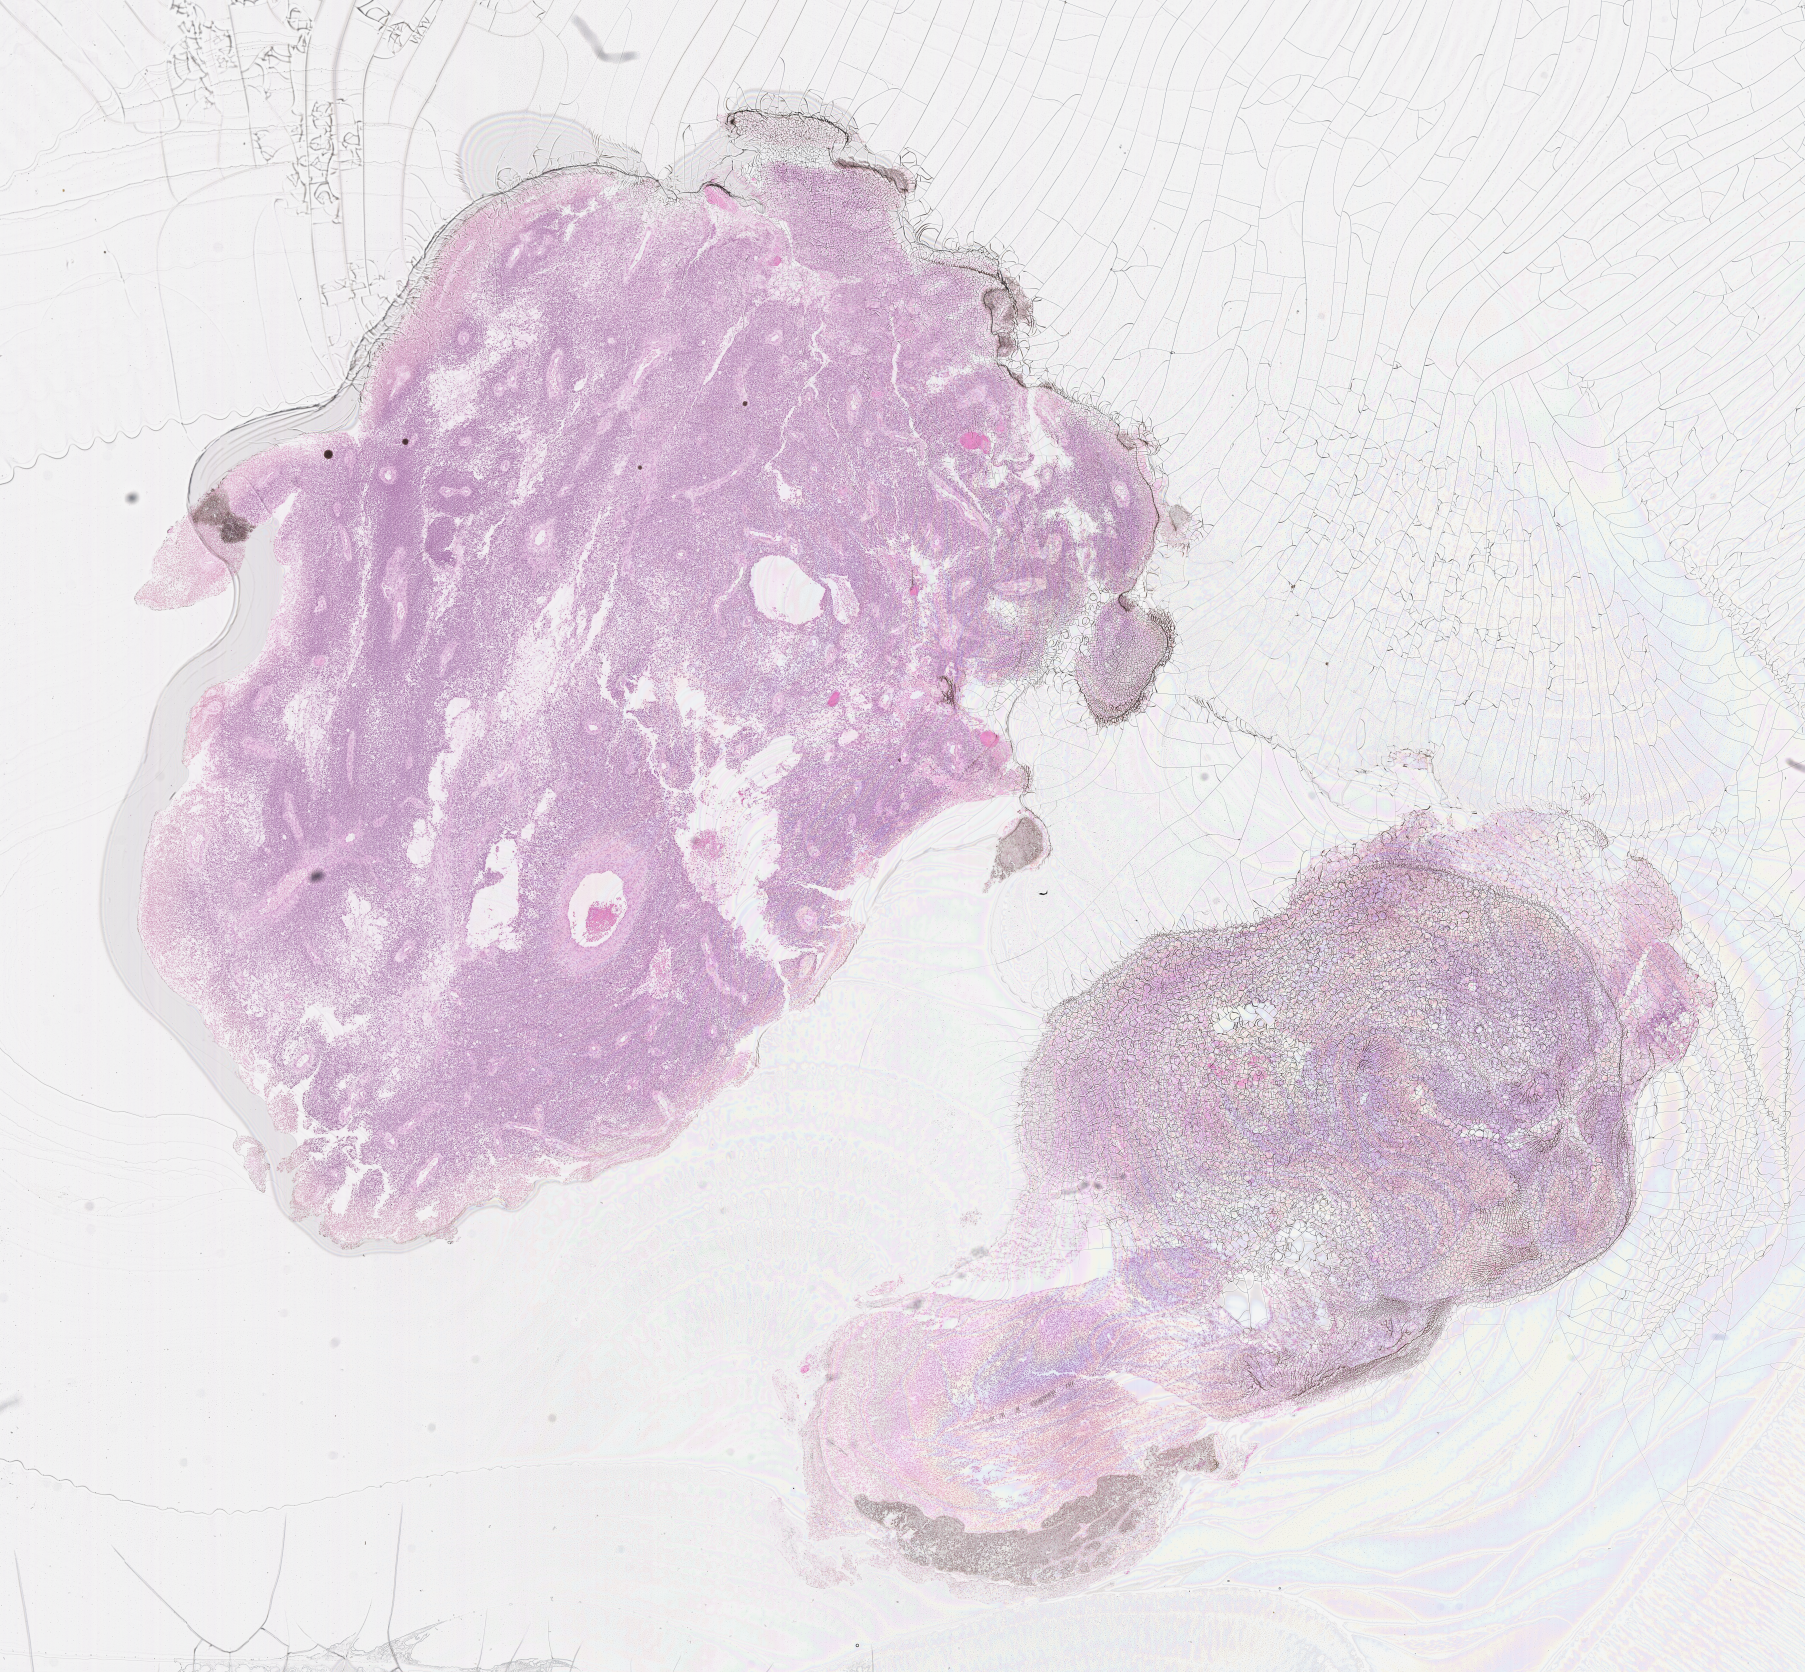
Digitized hematoxylin and eosin (H&E)-stained section of tumor tissue — shown as a low-resolution overview of the whole scanned area (about 14.6 x 13.5 mm); FFPE section; sample anatomic site: retroperitoneum. Female patient, age at diagnosis 2.3 years.
Diagnosis: rhabdomyosarcoma; histological classification: embryonal rhabdomyosarcoma.